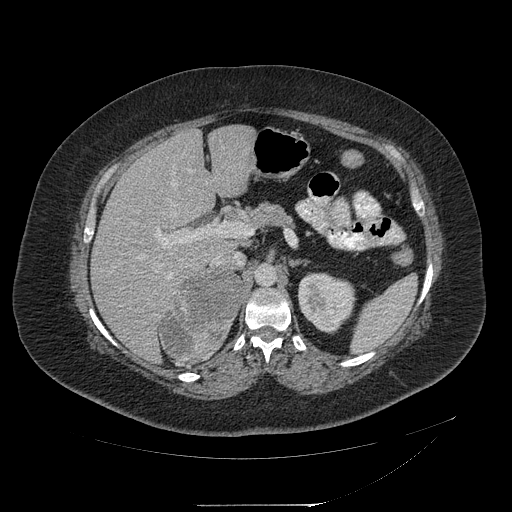
Contrast-enhanced abdominal CT, one axial slice. Position 131 of 217 along the scan axis. Reconstruction kernel STANDARD. Intravenous contrast given. Soft-tissue window (W 400 / L 40 HU). 1.25 mm slice thickness. 512 × 512 image matrix, field of view 453 × 453 mm. Female patient, age 55 years. Case-level facts recorded for this patient, not image findings: diagnosis: adrenocortical carcinoma; tumour side: right adrenal; tumour size at pathology: 11 cm; Ki-67 index: 20 %; stage (as recorded): 2.
Annotated regions visible in this slice (semi-automatic segmentation, software-assisted and operator-edited):
- mass: box from (x=161, y=270) to (x=243, y=361) px